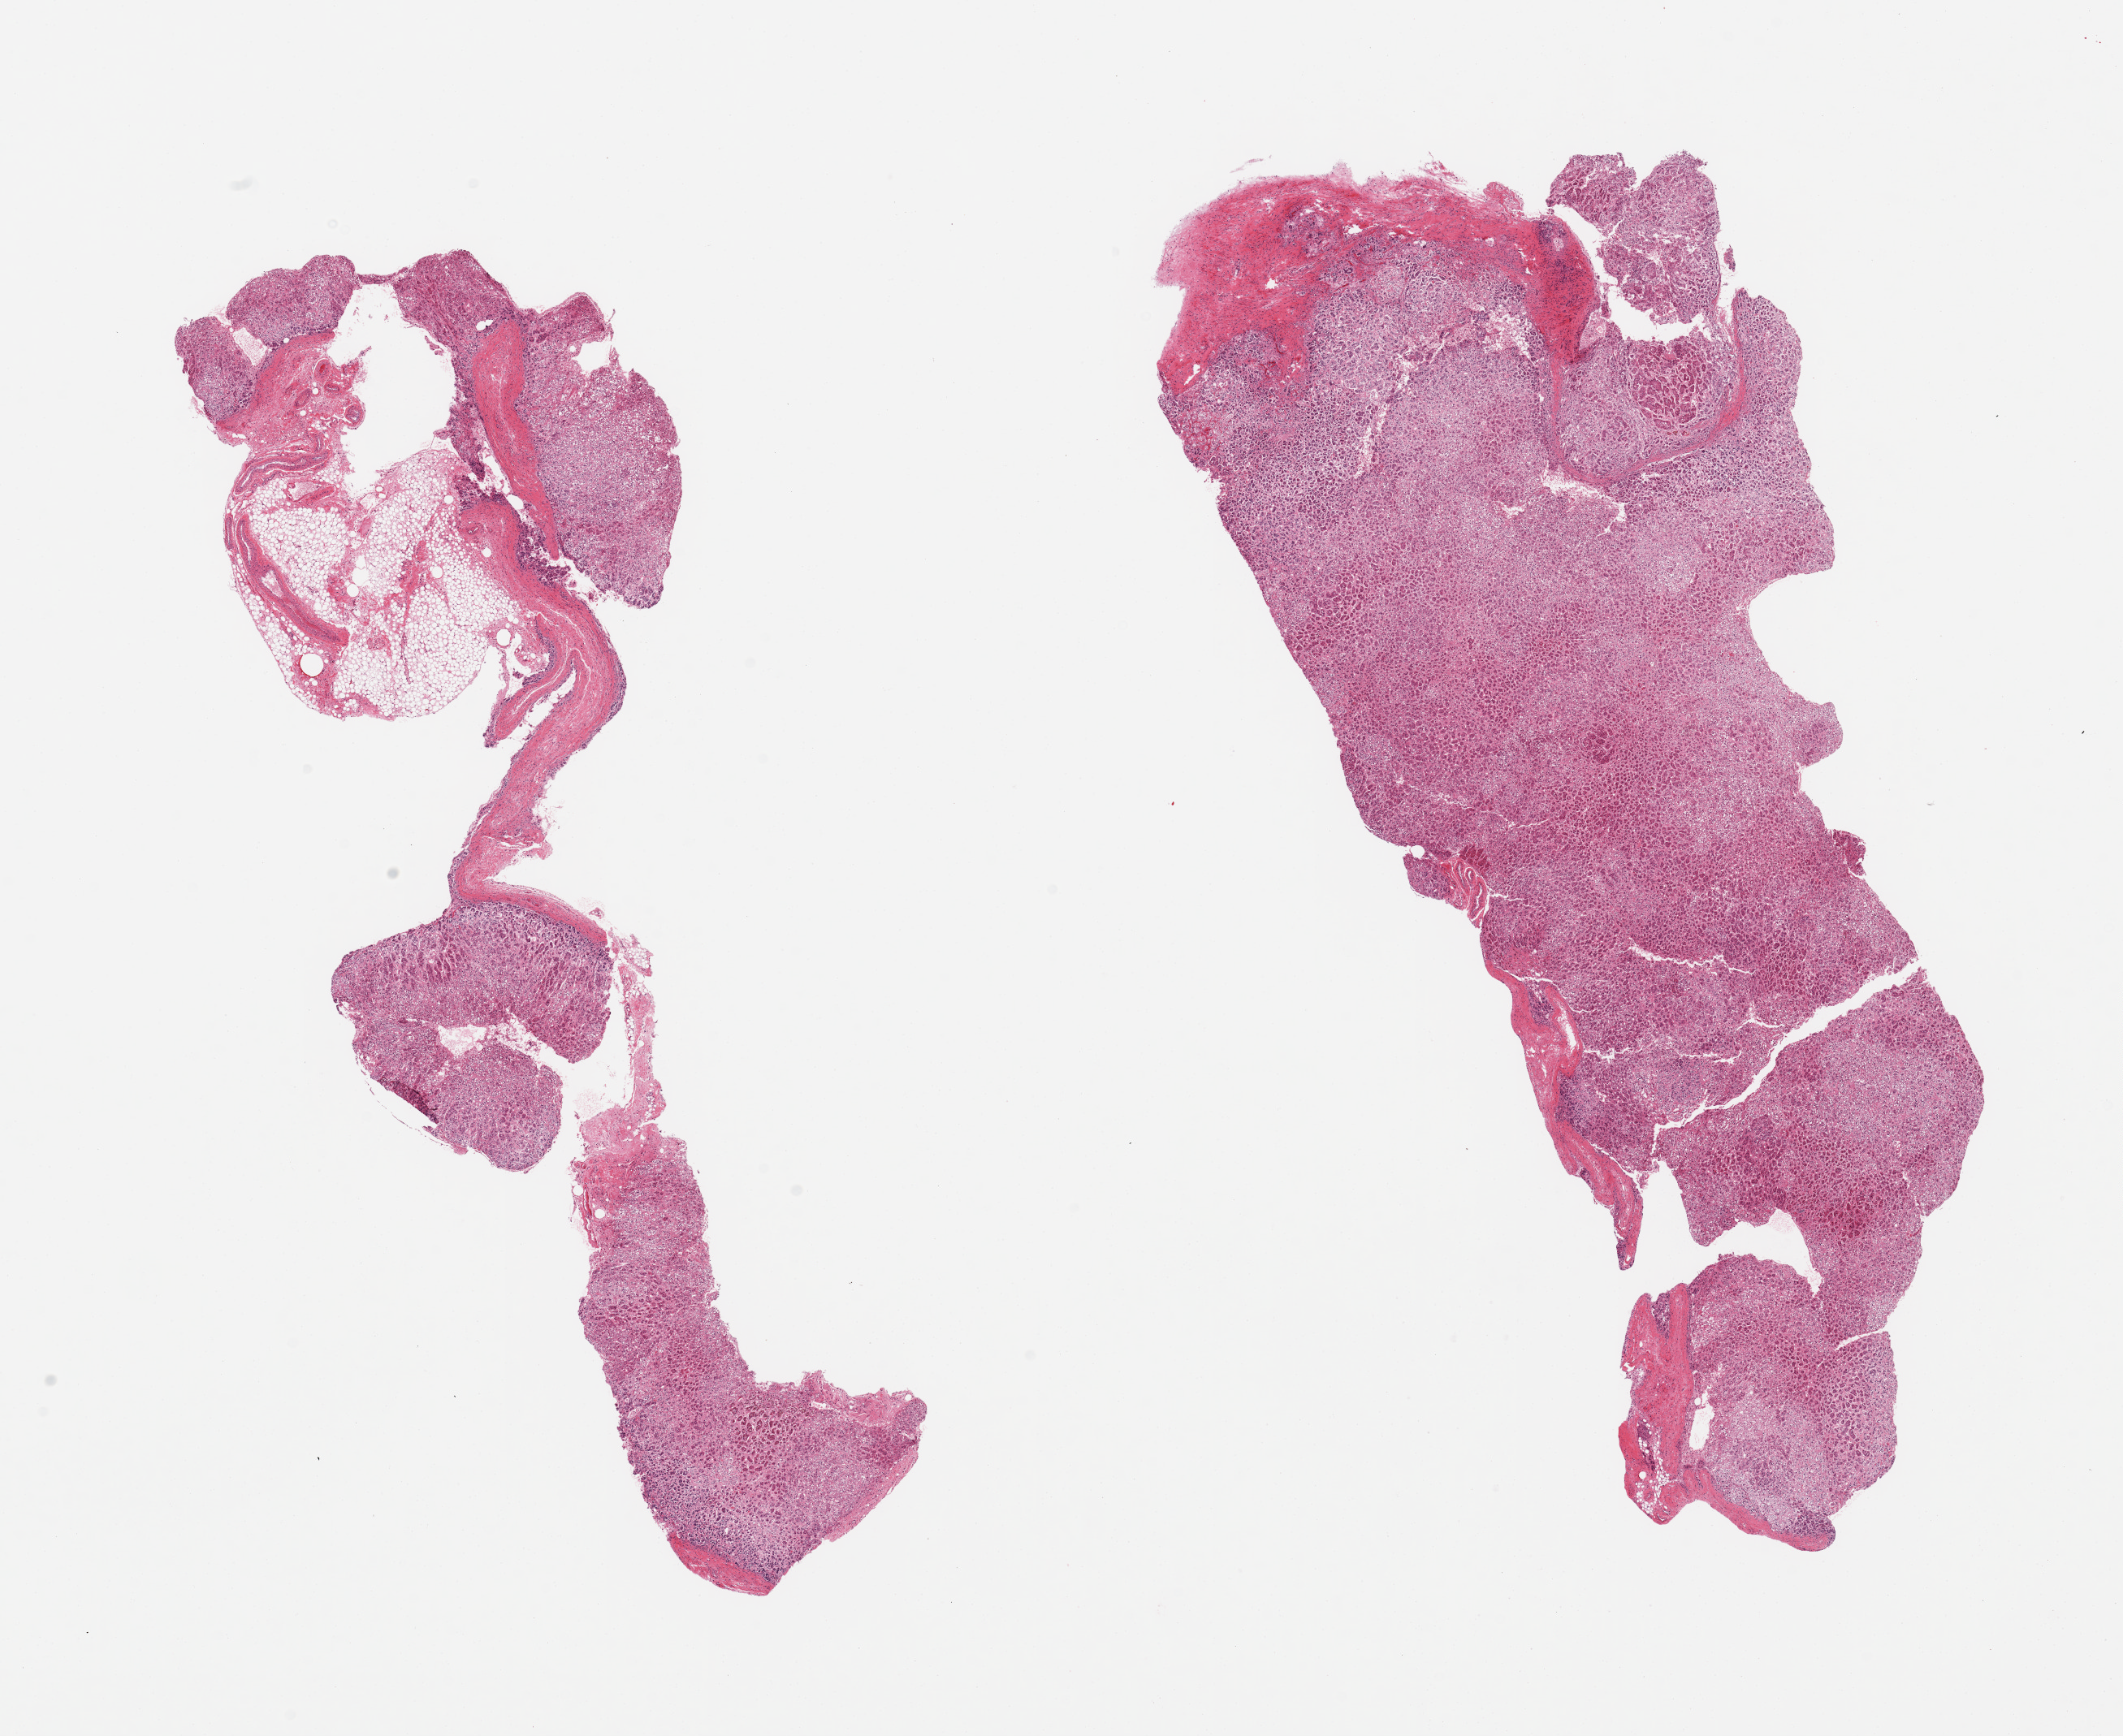
Haematoxylin and eosin whole-slide image, brightfield — low-resolution overview of the scanned area, about 20.7 x 16.9 mm (slide scanned at 20x); PAXgene-fixed paraffin-embedded (PFPE) section; sampled site (target tissue): adrenal gland; donor tissue sample. Donor: female.
Review note (as recorded): 2 pieces, autolysis moderately advanced; adherent fat is ~10% of specimen.